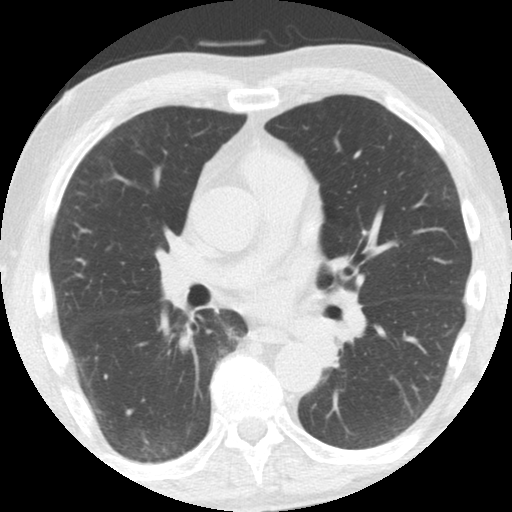
Chest CT (low-dose screening protocol), one axial image. Third screening round (two years after baseline). Lung window (W 1500 / L -600 HU). Standard (soft-tissue) reconstruction kernel (STANDARD). 512 × 512 image matrix. Male participant, aged 61 years at enrolment. Former smoker at enrolment.
Lesion marked by an expert reader, bounding box <295,316,344,362> (left, top, right, bottom; pixels). No non-calcified nodule or mass ≥4 mm was recorded by the screening reader at this exam. Later outcome: lung cancer diagnosed 363 days after this screen — squamous cell carcinoma, NOS, left upper lobe, left lower lobe, well differentiated (G1), stage IIB (AJCC 6th edition), 100 mm at pathology.